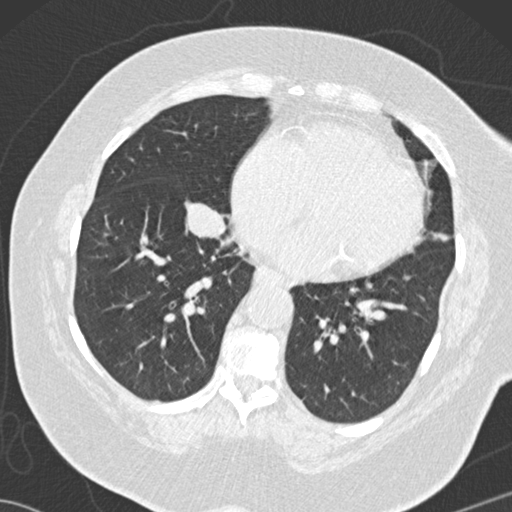
Low-dose screening chest CT, one axial slice. Position 51 of 146 along the scan axis. Reconstruction kernel B30f. 120 kVp. Lung window (W 1500 / L -600 HU). 2 mm slice thickness. 512 × 512 image matrix, field of view 350 × 350 mm.
Outlined on this slice (outlined manually by an expert reader):
- lesion 3 (tumor, lower lobe of right lung): bounding box <187,203,228,237> (left, top, right, bottom; pixels)